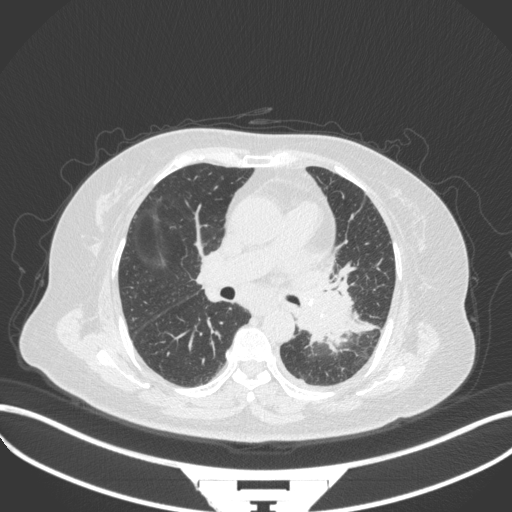
Chest CT, one axial slice. Position 194 of 328 along the scan axis. Reconstruction kernel B31f. Lung window (W 1500 / L -600 HU). 512 × 512 image matrix, field of view 400 × 400 mm. Patient: female, 69 years. Case-level facts recorded for this patient, not image findings: clinical TNM (as recorded): T2b N3 M1.
Structures marked on this image (rectangle marked by the reading radiologist):
- lung tumour (recorded histology: adenocarcinoma): bounding box (x1, y1, x2, y2) in pixels: (287, 265, 369, 354)